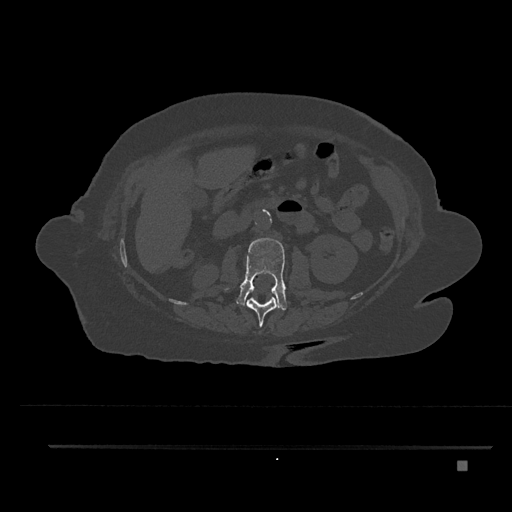
CT including the spine, one axial slice; slice 191 of 797 in the series (ordered by position); 120 kVp; bone window (W 1800 / L 400 HU); 0.5 mm slice thickness; 512 × 512 image matrix, field of view 437 × 437 mm. Patient: female, 76 years. Case-level facts recorded for this patient, not image findings: primary cancer: lung; vertebrae with lytic lesions (as recorded): T11, L3.
Annotated regions visible in this slice (semi-automatic segmentation, software-assisted and operator-edited):
- L1 vertebra: bounding box <246,297,279,327> (left, top, right, bottom; pixels)
- L2 vertebra: <237,237,287,311>